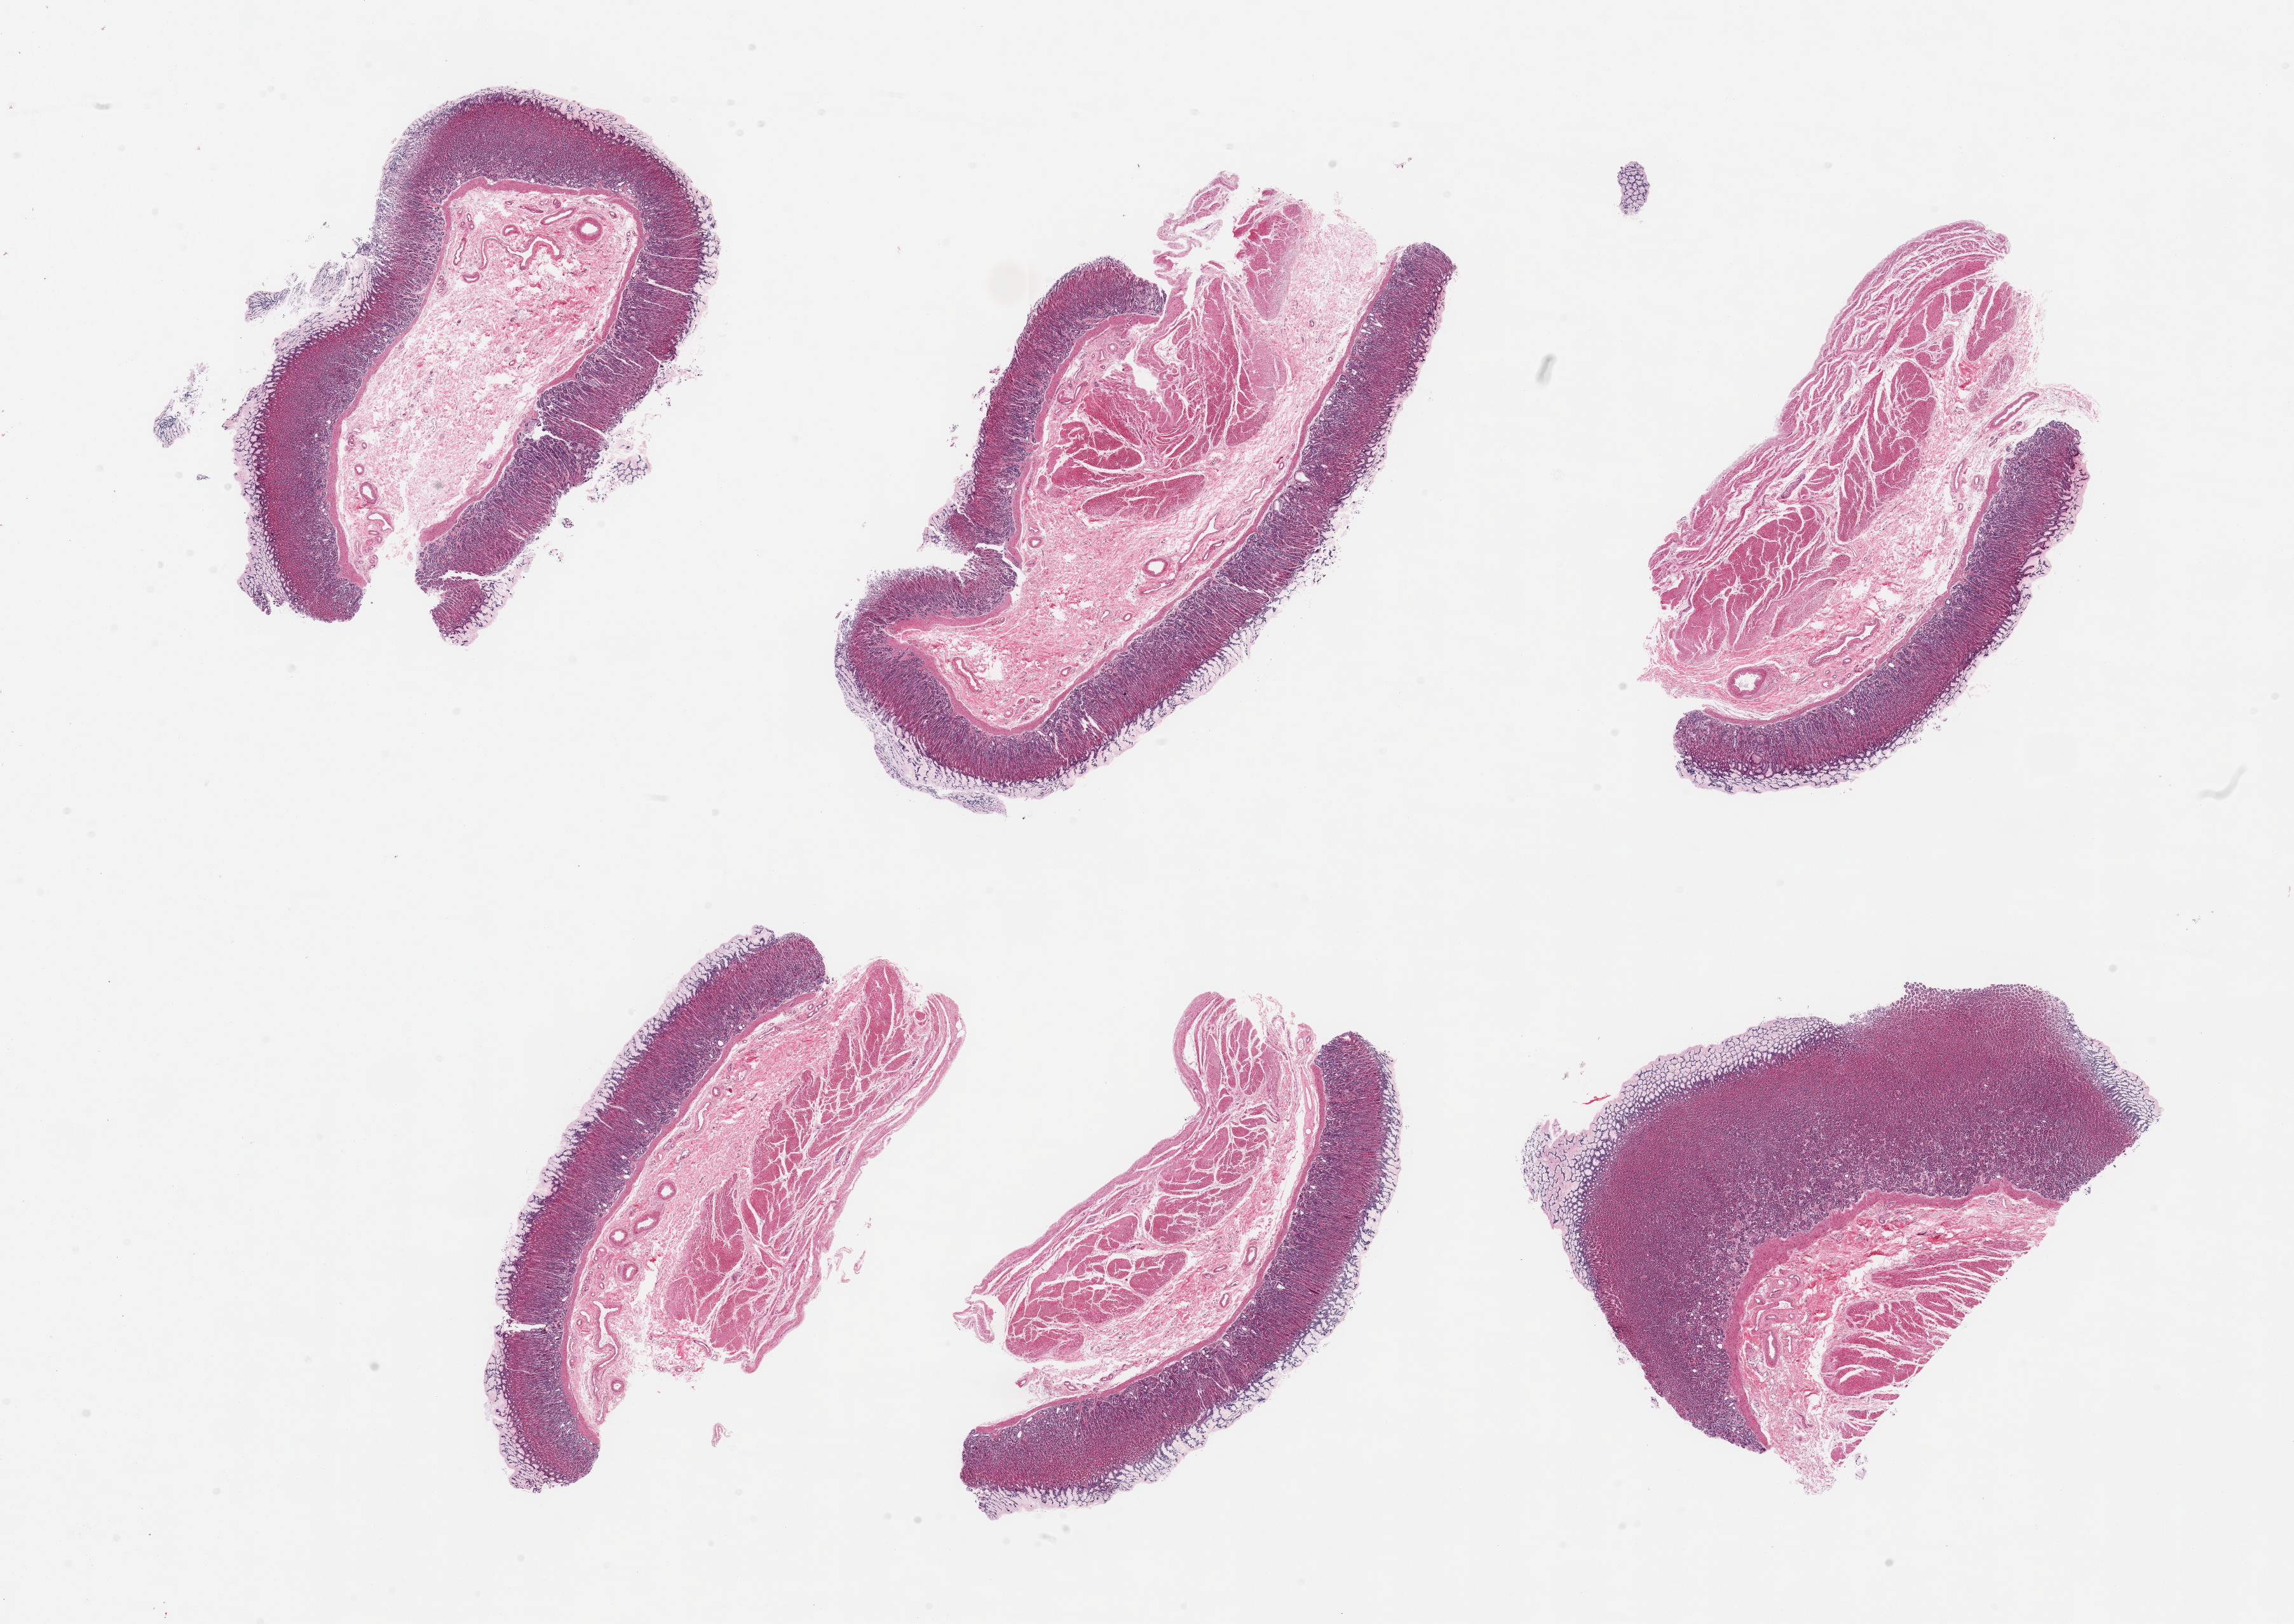
Haematoxylin and eosin whole-slide image, brightfield, whole scanned area (about 28.5 x 20.2 mm) shown as a low-resolution overview; PAXgene-fixed paraffin-embedded (PFPE) section; sampled site (target tissue): stomach; tissue donor sample. Female donor.
Pathologist's review note for this sample: 6 pieces; 5 have full thickness wall; mild basal microcystic glands.